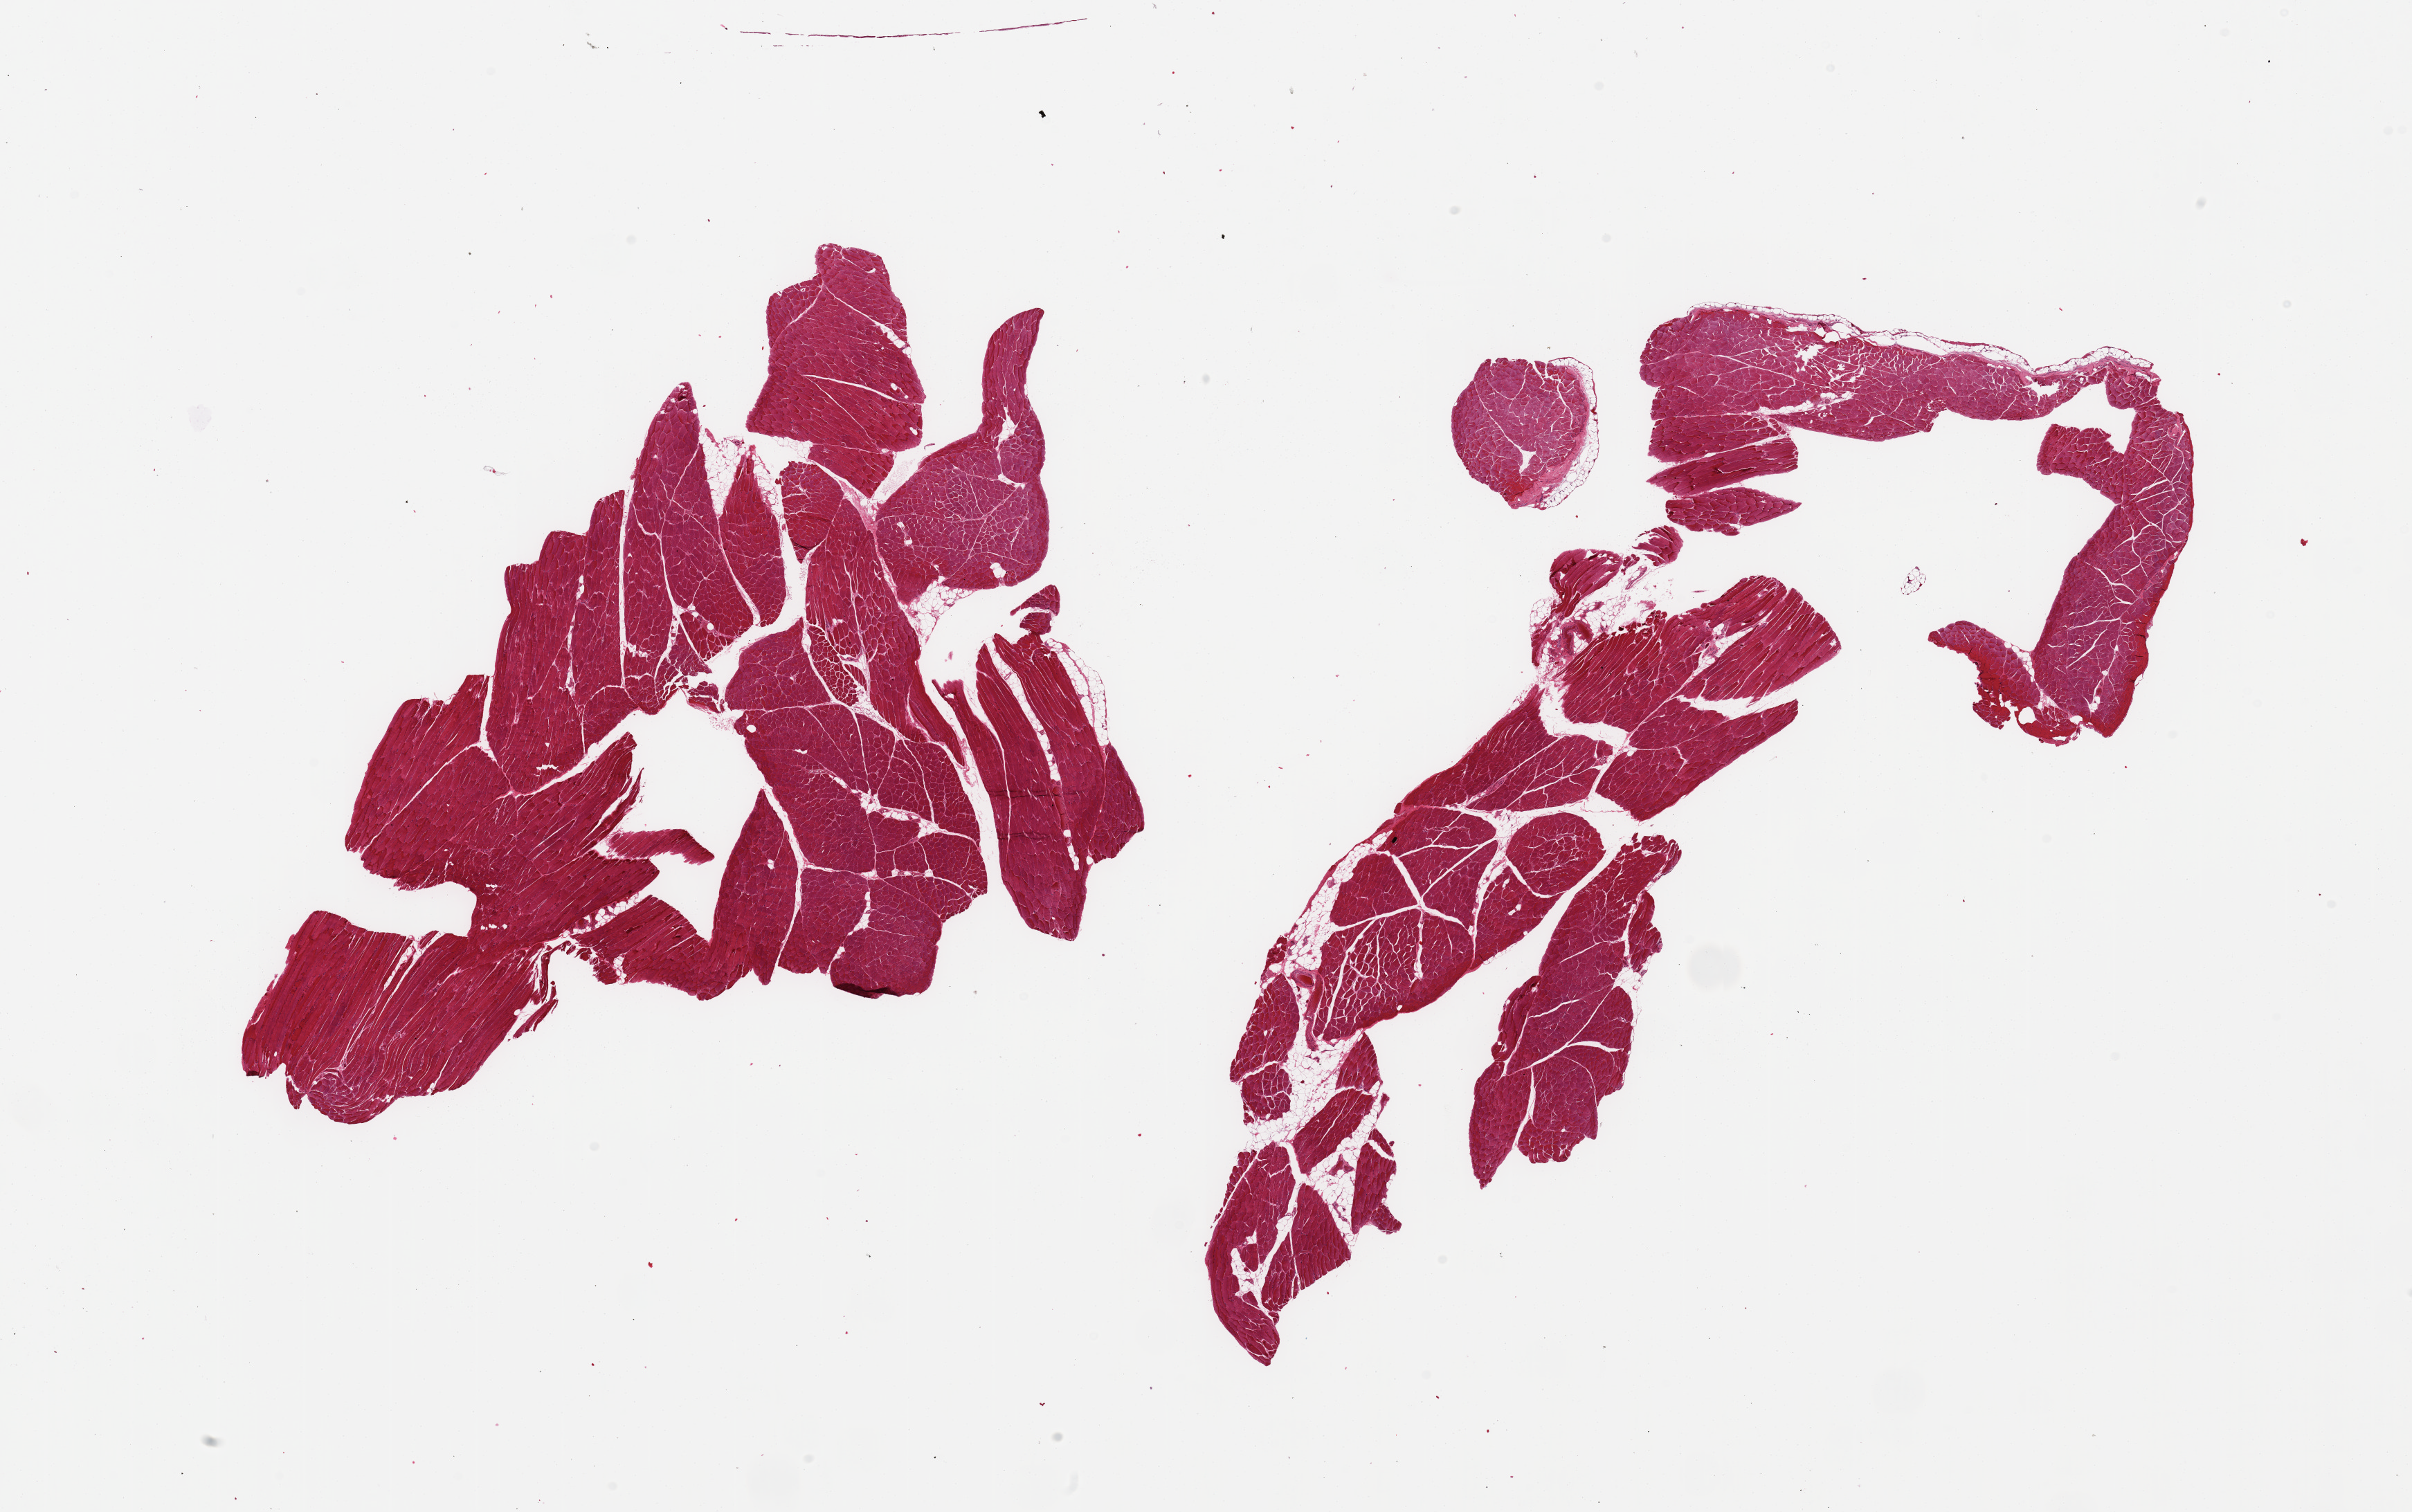
Whole-slide image, haematoxylin and eosin stain, brightfield — a low-resolution overview of the entire scanned area, about 27.6 x 17.3 mm; PAXgene-fixed paraffin-embedded (PFPE) section; target tissue: skeletal muscle; donor tissue sample. Donor: female.
• pathologist's review note for this sample: 2 pieces, trace interstitial fat